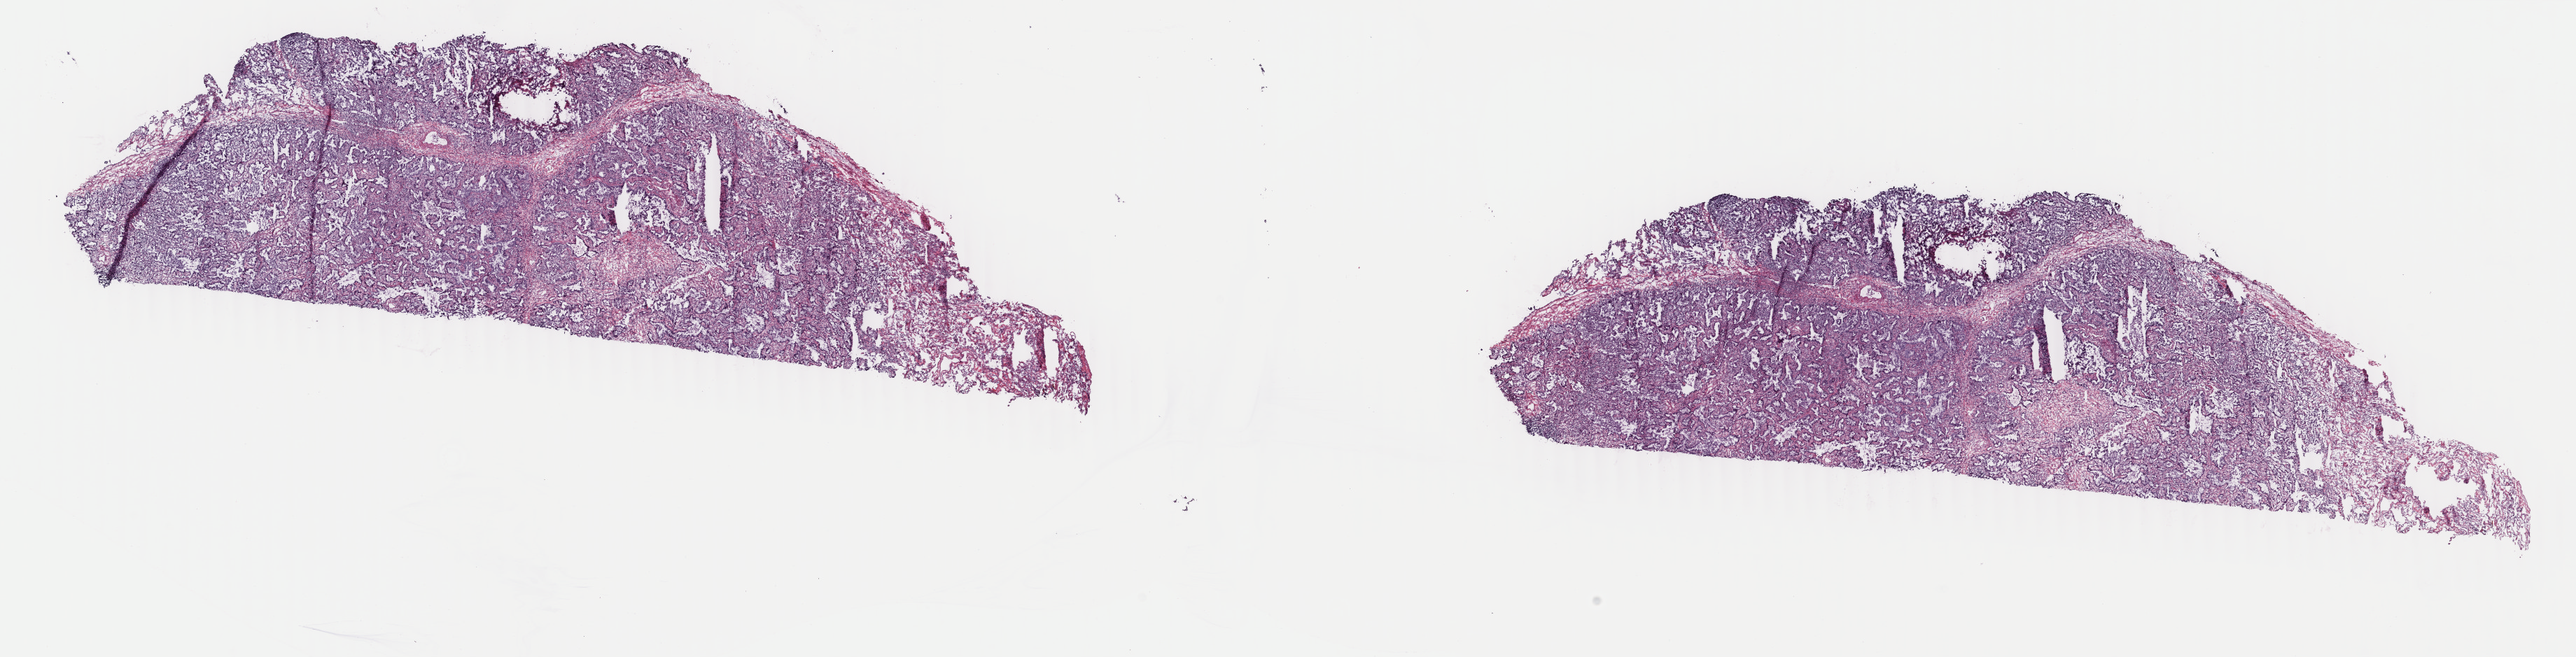
Hematoxylin and eosin (H&E) stained whole-slide image, low-resolution overview of the scanned area, about 29.3 x 7.5 mm; frozen section from the top of the tissue portion; sample: primary tumour, lung. Female patient; age at initial diagnosis 60 years. Composition of this section per pathologist review: tumour cells 100%, tumour nuclei 65%, normal cells 0%, stromal cells 0%, necrosis 0%. Inflammatory infiltration, as recorded: lymphocyte infiltration 5%, monocyte infiltration 1%, neutrophil infiltration 0%.
AJCC pathologic stage: IB (7th edition). Laterality: right. Histologic diagnosis: Adenocarcinoma with mixed subtypes (upper lobe, lung).